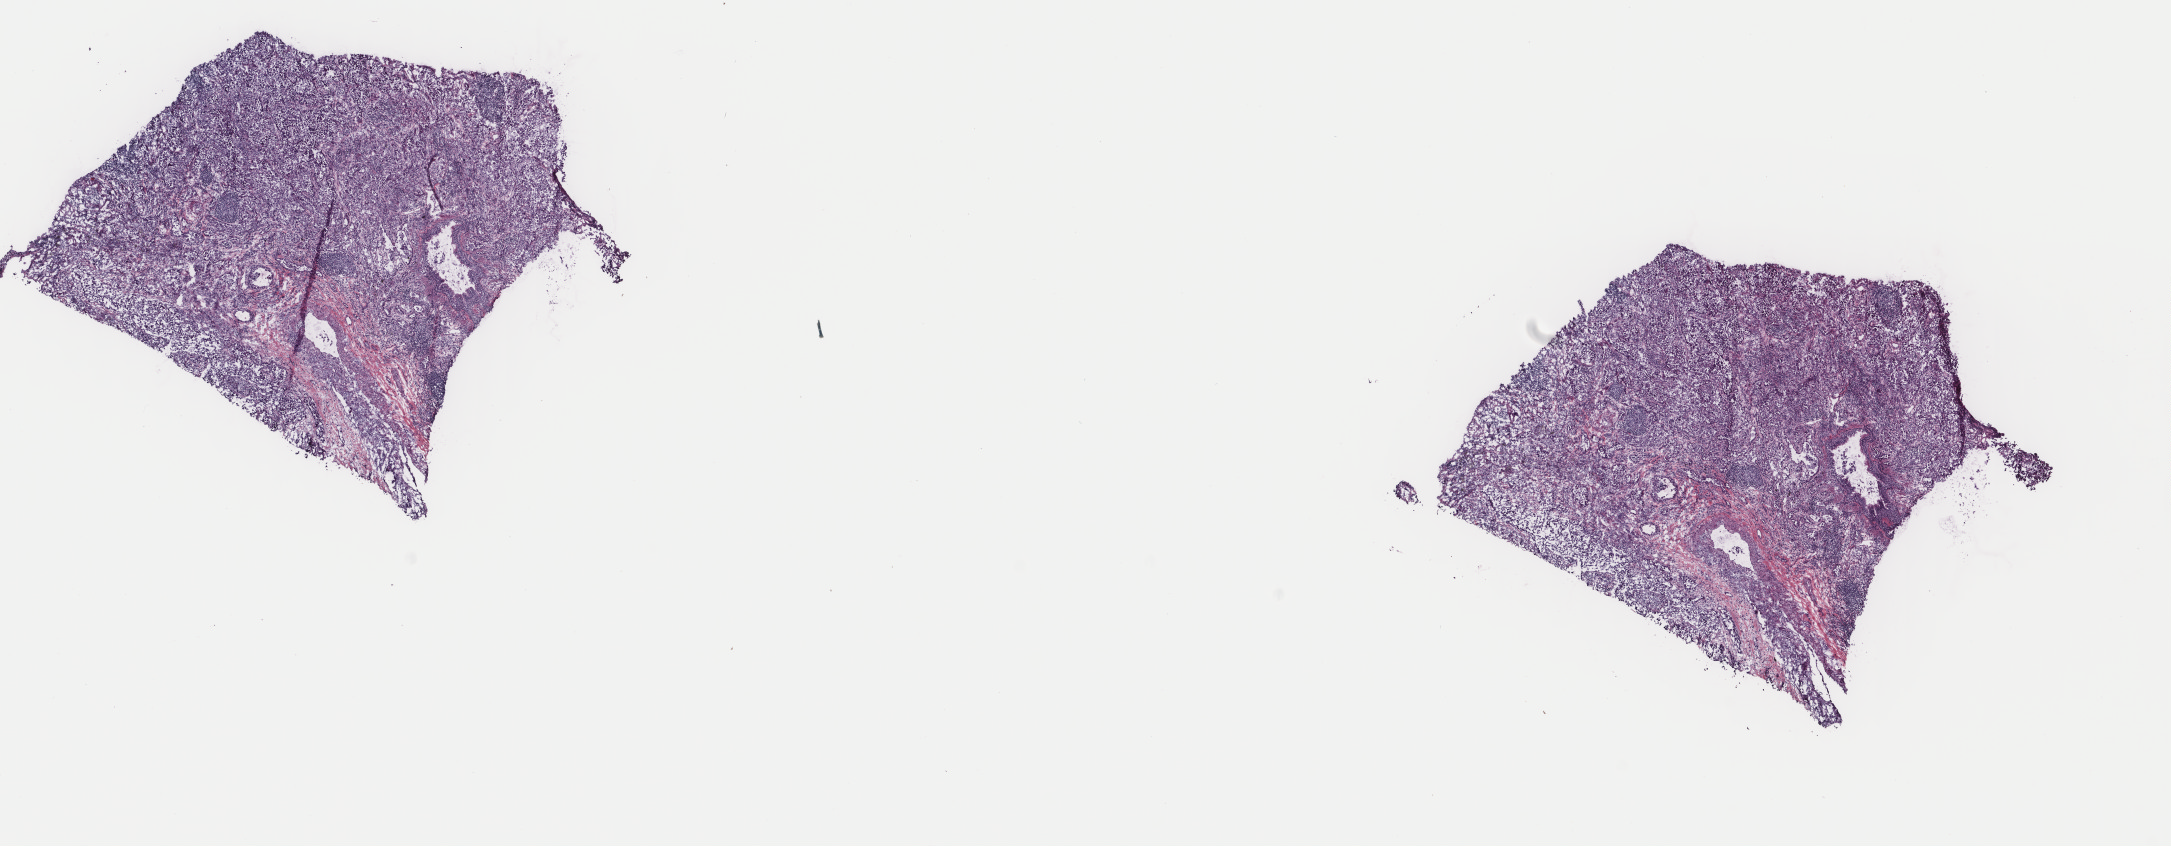
H&E whole-slide image — shown as a low-resolution overview of the whole scanned area (about 17.2 x 6.7 mm, acquisition: 40x scan). Frozen section. Primary tumour sample from the lung. Patient: female, age at initial diagnosis 54 years. Composition of this section per pathologist review: tumour cells 100%, tumour nuclei 60%, normal cells 0%, stromal cells 0%, necrosis 0%. Infiltration values recorded for this section: lymphocyte infiltration 20%, monocyte infiltration 0%, neutrophil infiltration 0%.
• AJCC pathologic stage: IB (6th edition)
• pathologic diagnosis: Adenocarcinoma with mixed subtypes (lower lobe, lung)
• TNM: T2 N0 M0